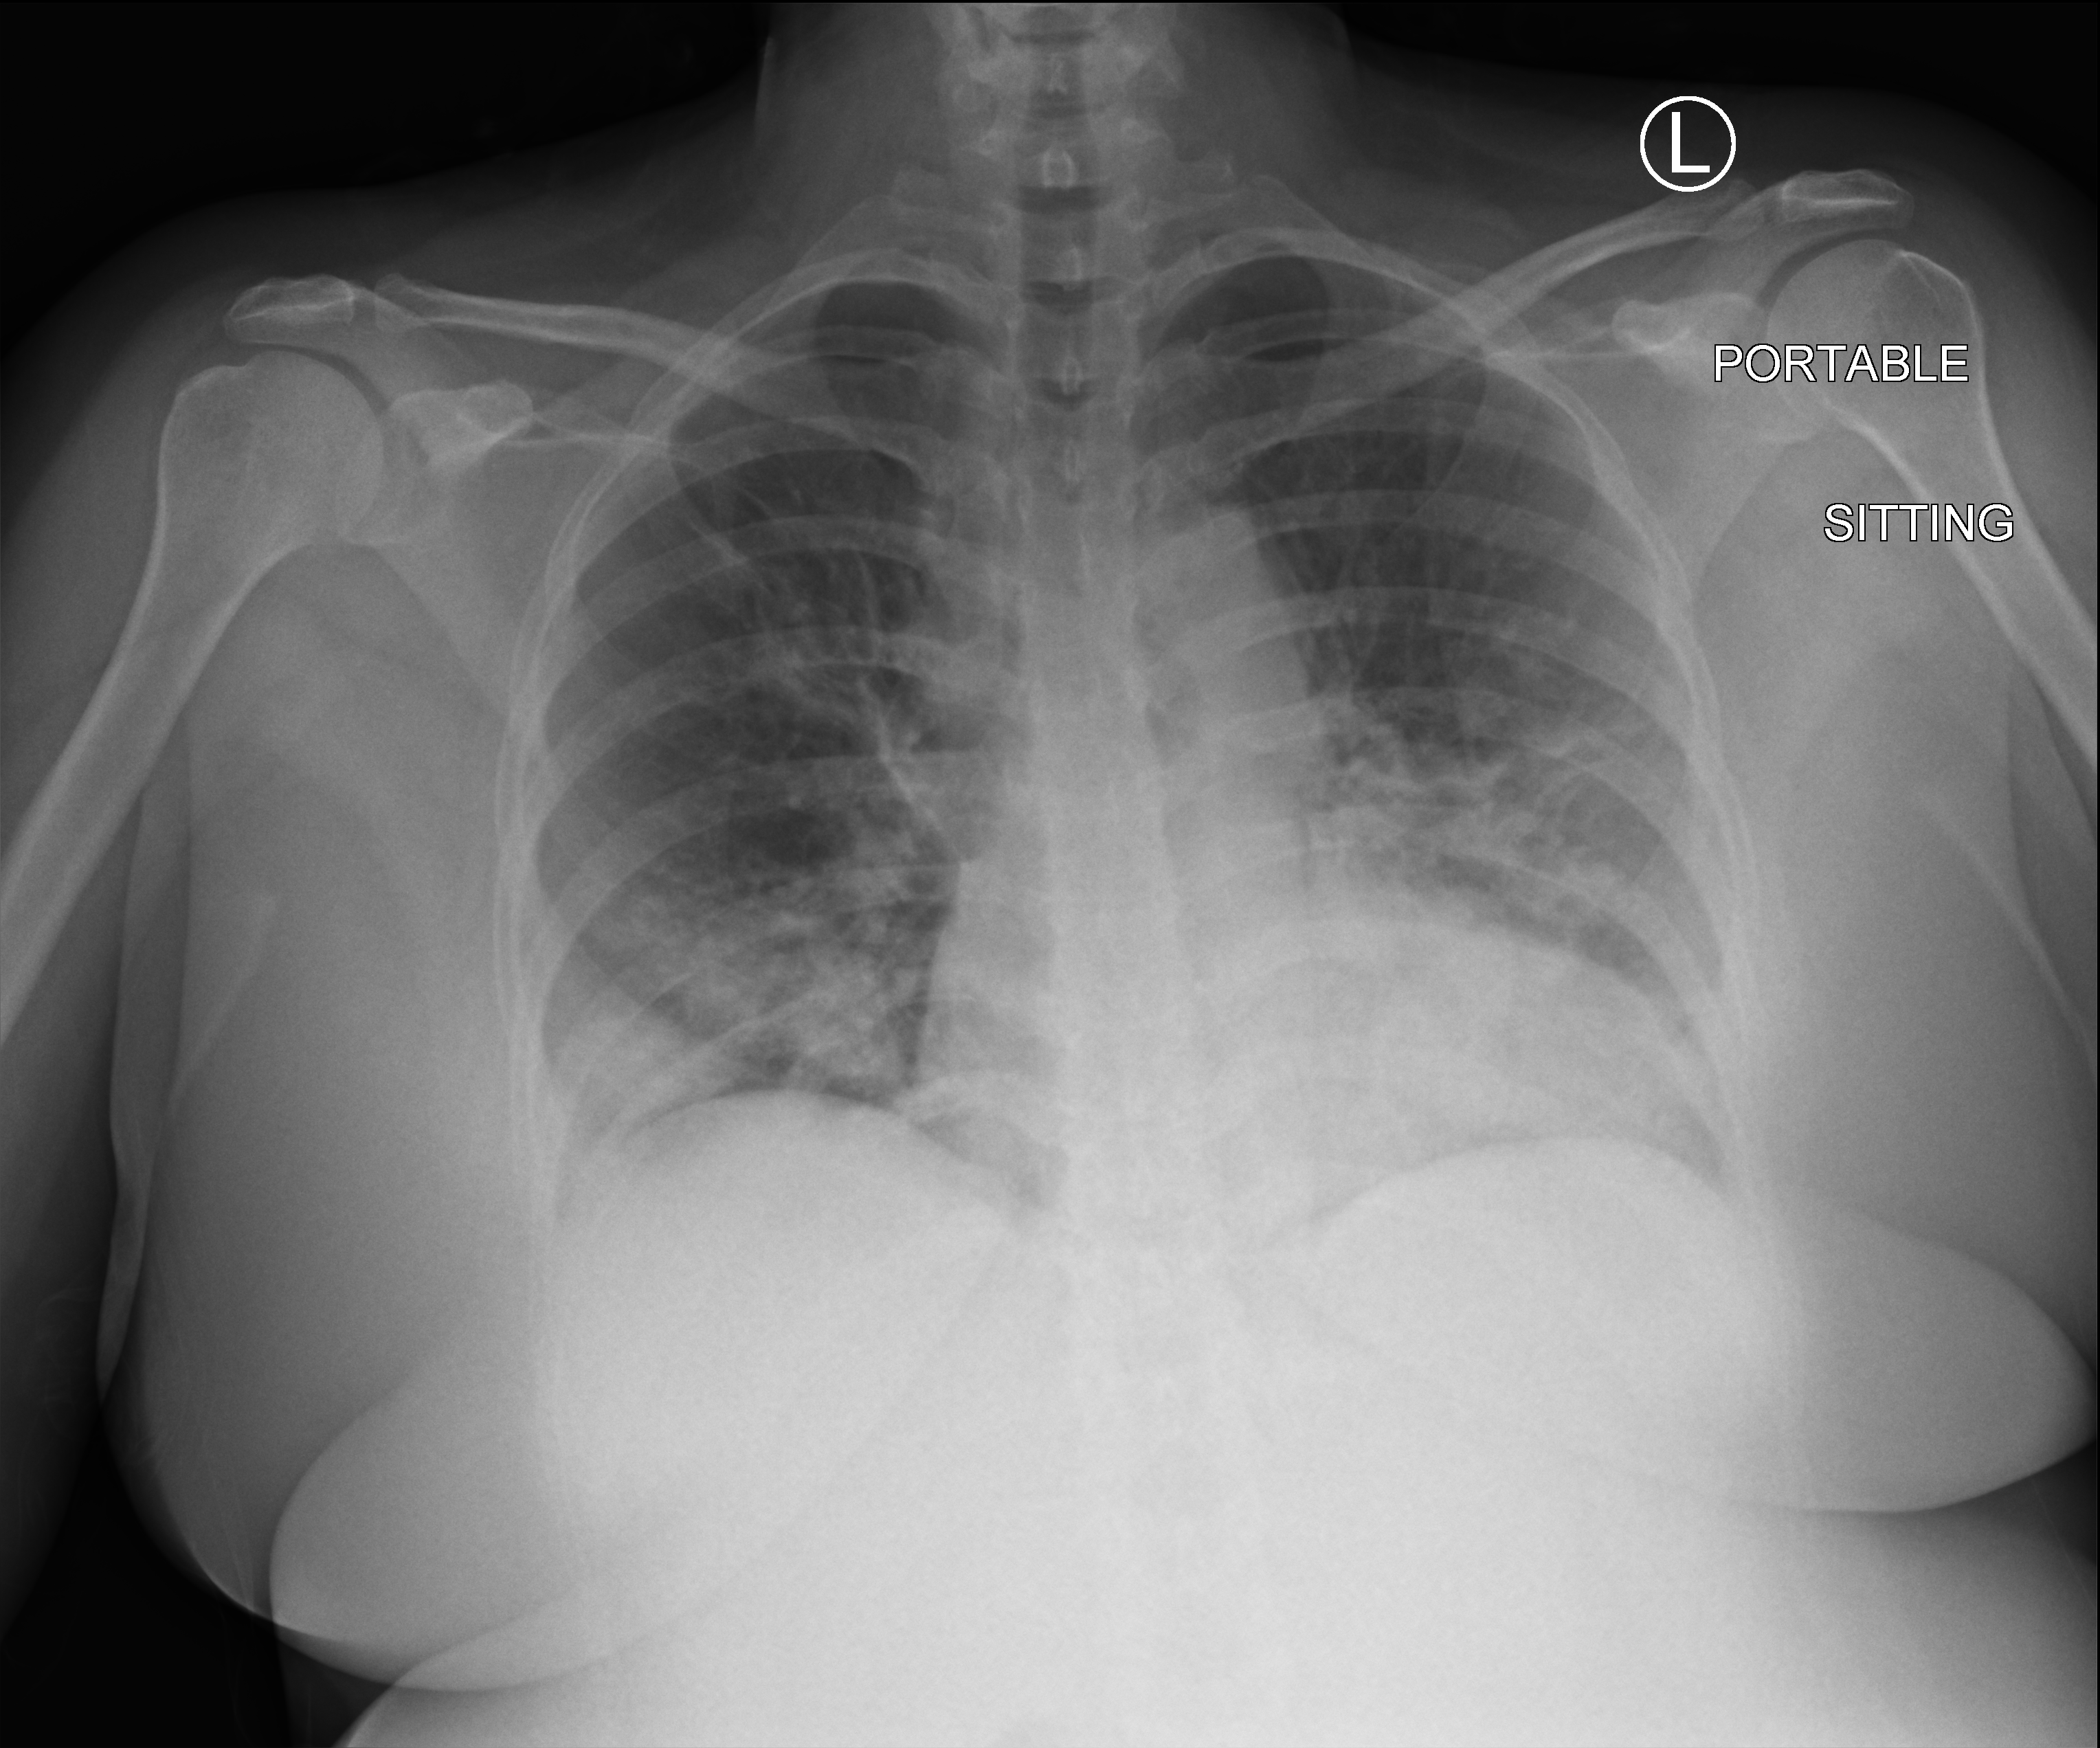
Chest X-ray (portable), anteroposterior (AP) projection. Female patient hospitalised with COVID-19, age 18–59 years.
Admission-level facts for this patient (not findings on this image; timing relative to this image not recorded): mechanically ventilated during this hospital stay: no; admitted to intensive care during this hospital stay: no.